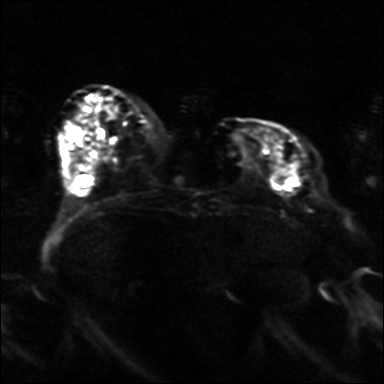
Breast MRI, one axial slice; position 10 of 36 along the scan axis; diffusion-weighted series; image 2 of 4 stored at this slice position (different b-values; order by instance number); 3 T; 4 mm slice thickness; 384 × 384 image matrix, field of view 320 × 320 mm. Female patient.
Annotated regions visible in this slice (outlined manually by an expert reader):
- tumour on diffusion-weighted imaging: bounding box <275,164,299,177> (left, top, right, bottom; pixels)